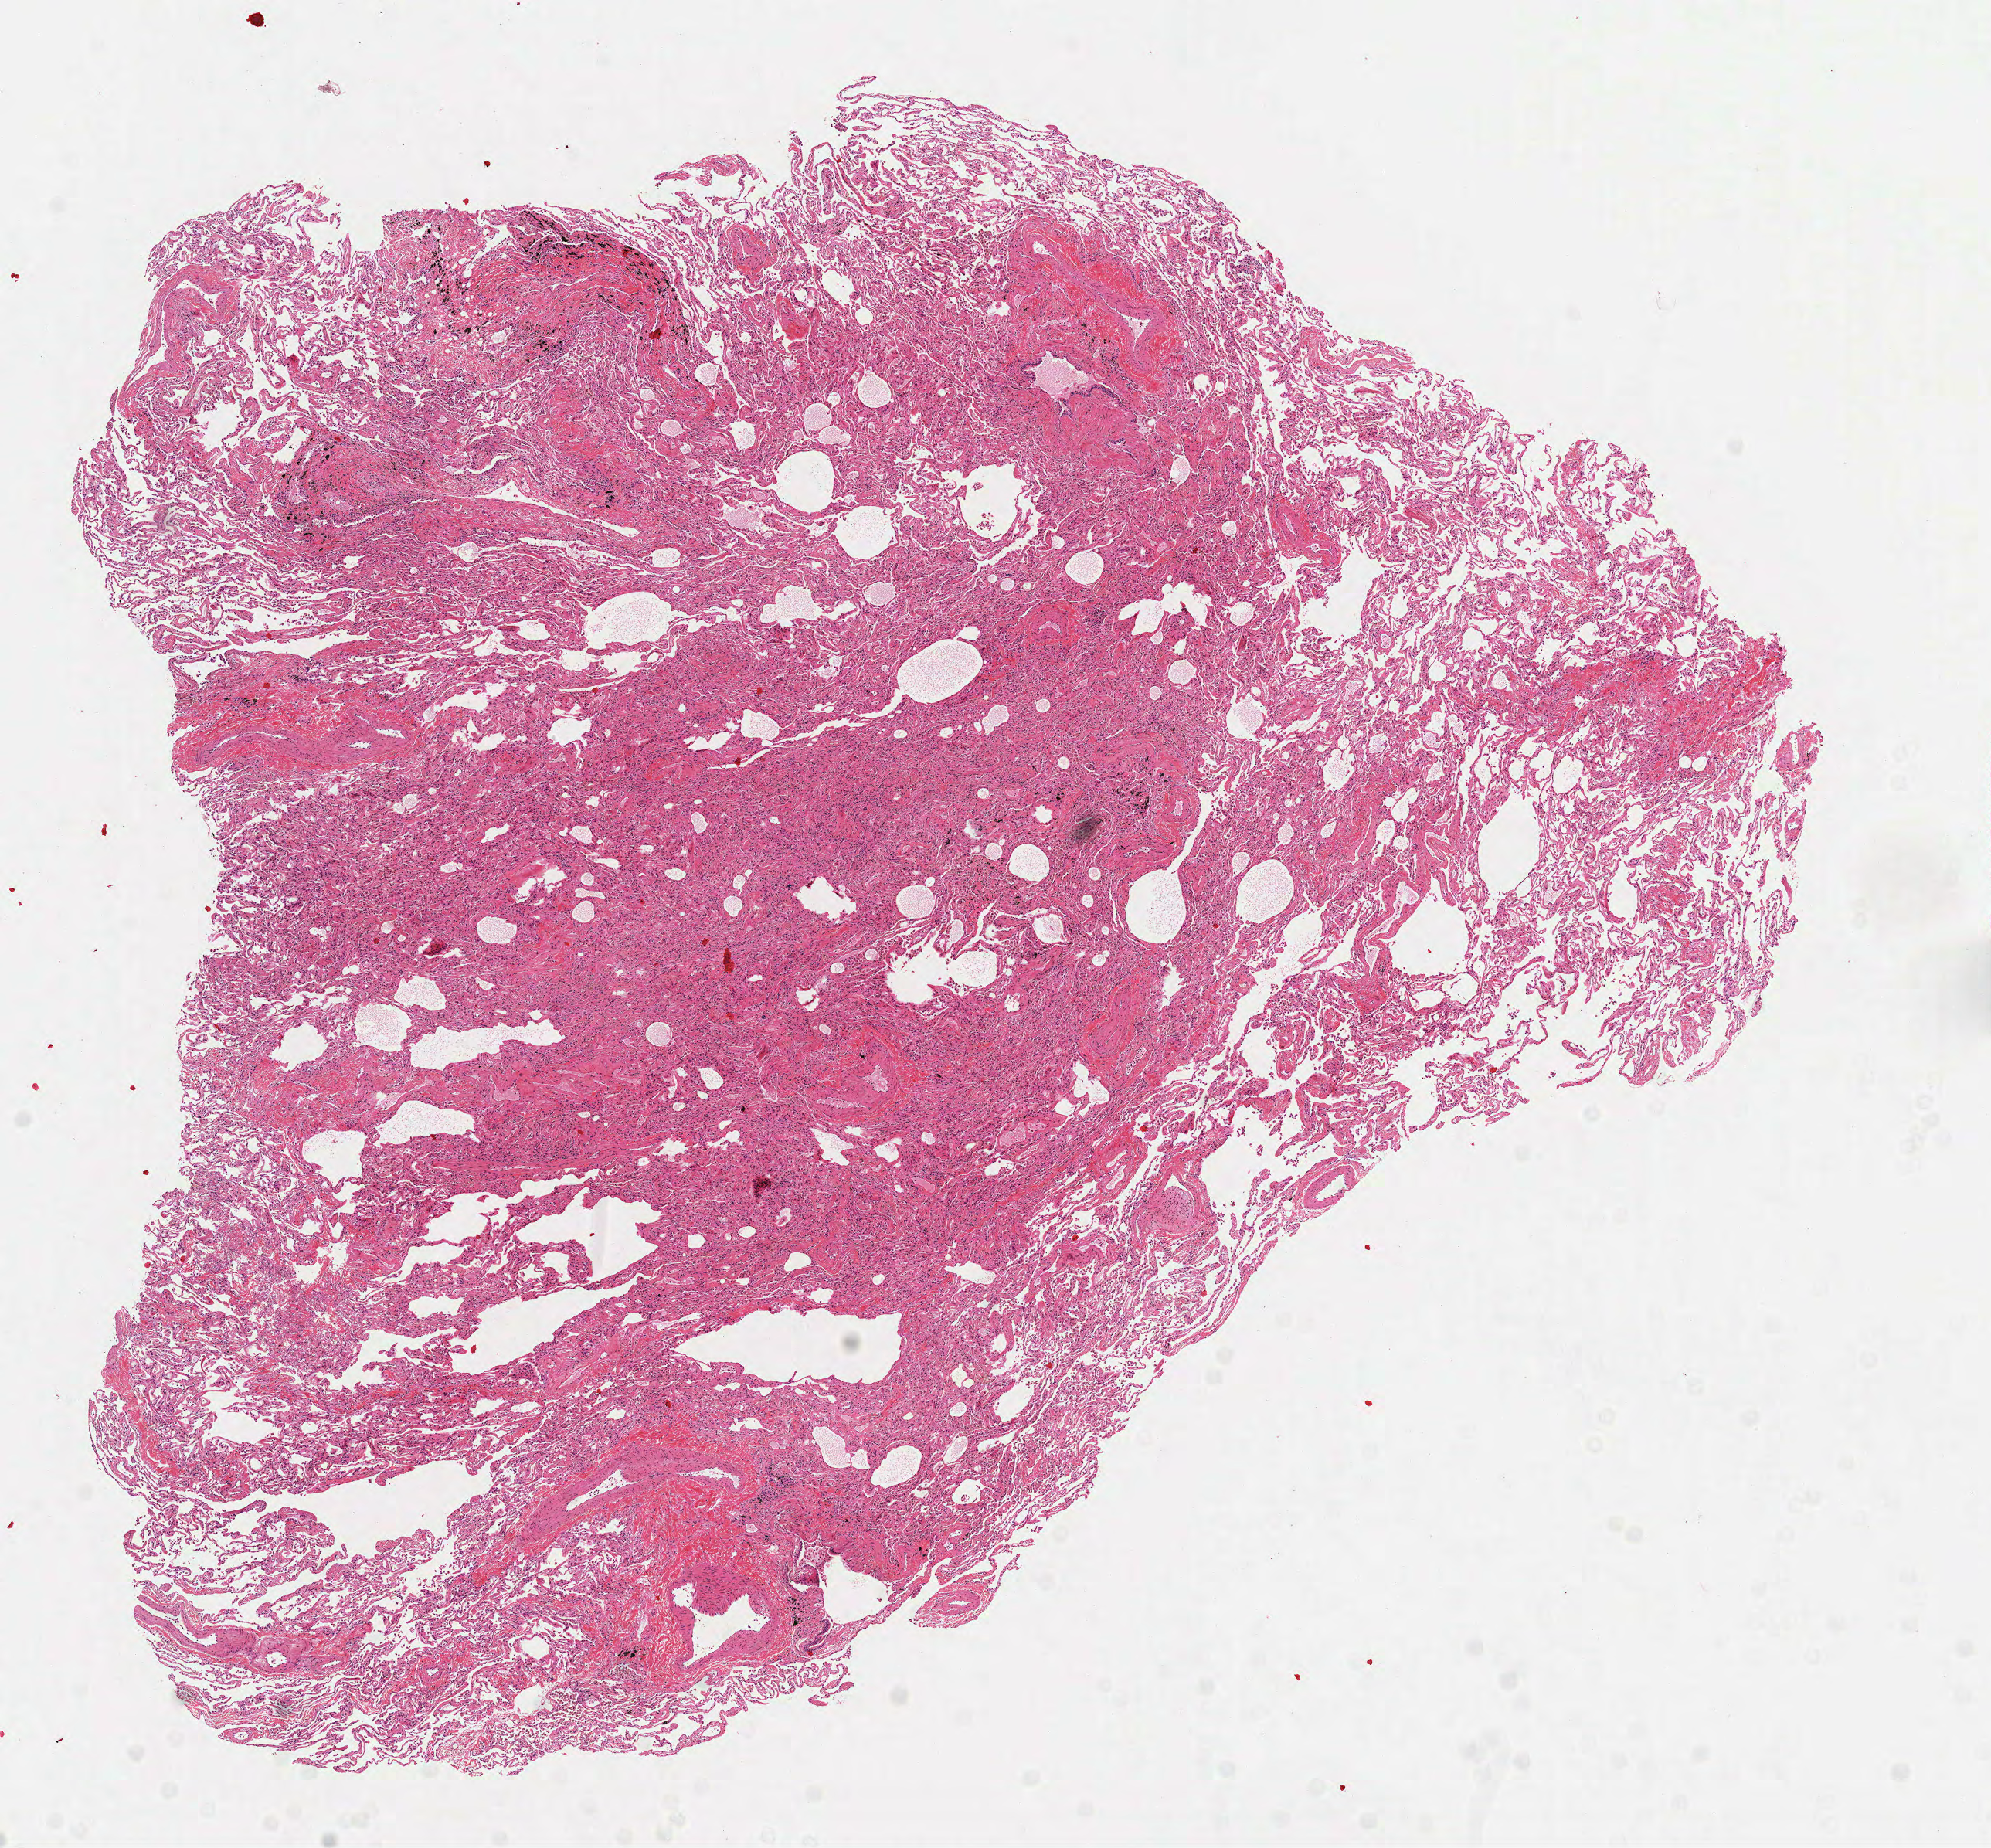
Digitized H&E-stained tissue section (whole slide) — shown as a low-resolution overview of the whole scanned area (about 10.4 x 9.6 mm, acquisition: 40x scan). Frozen section from the top of the tissue portion. Lung, solid tissue normal (non-tumour tissue) sample. Male patient; age at initial diagnosis 56 years.
This section: solid tissue normal (non-tumour) sample from the same patient. Patient diagnosis: Adenocarcinoma, NOS (upper lobe, lung).